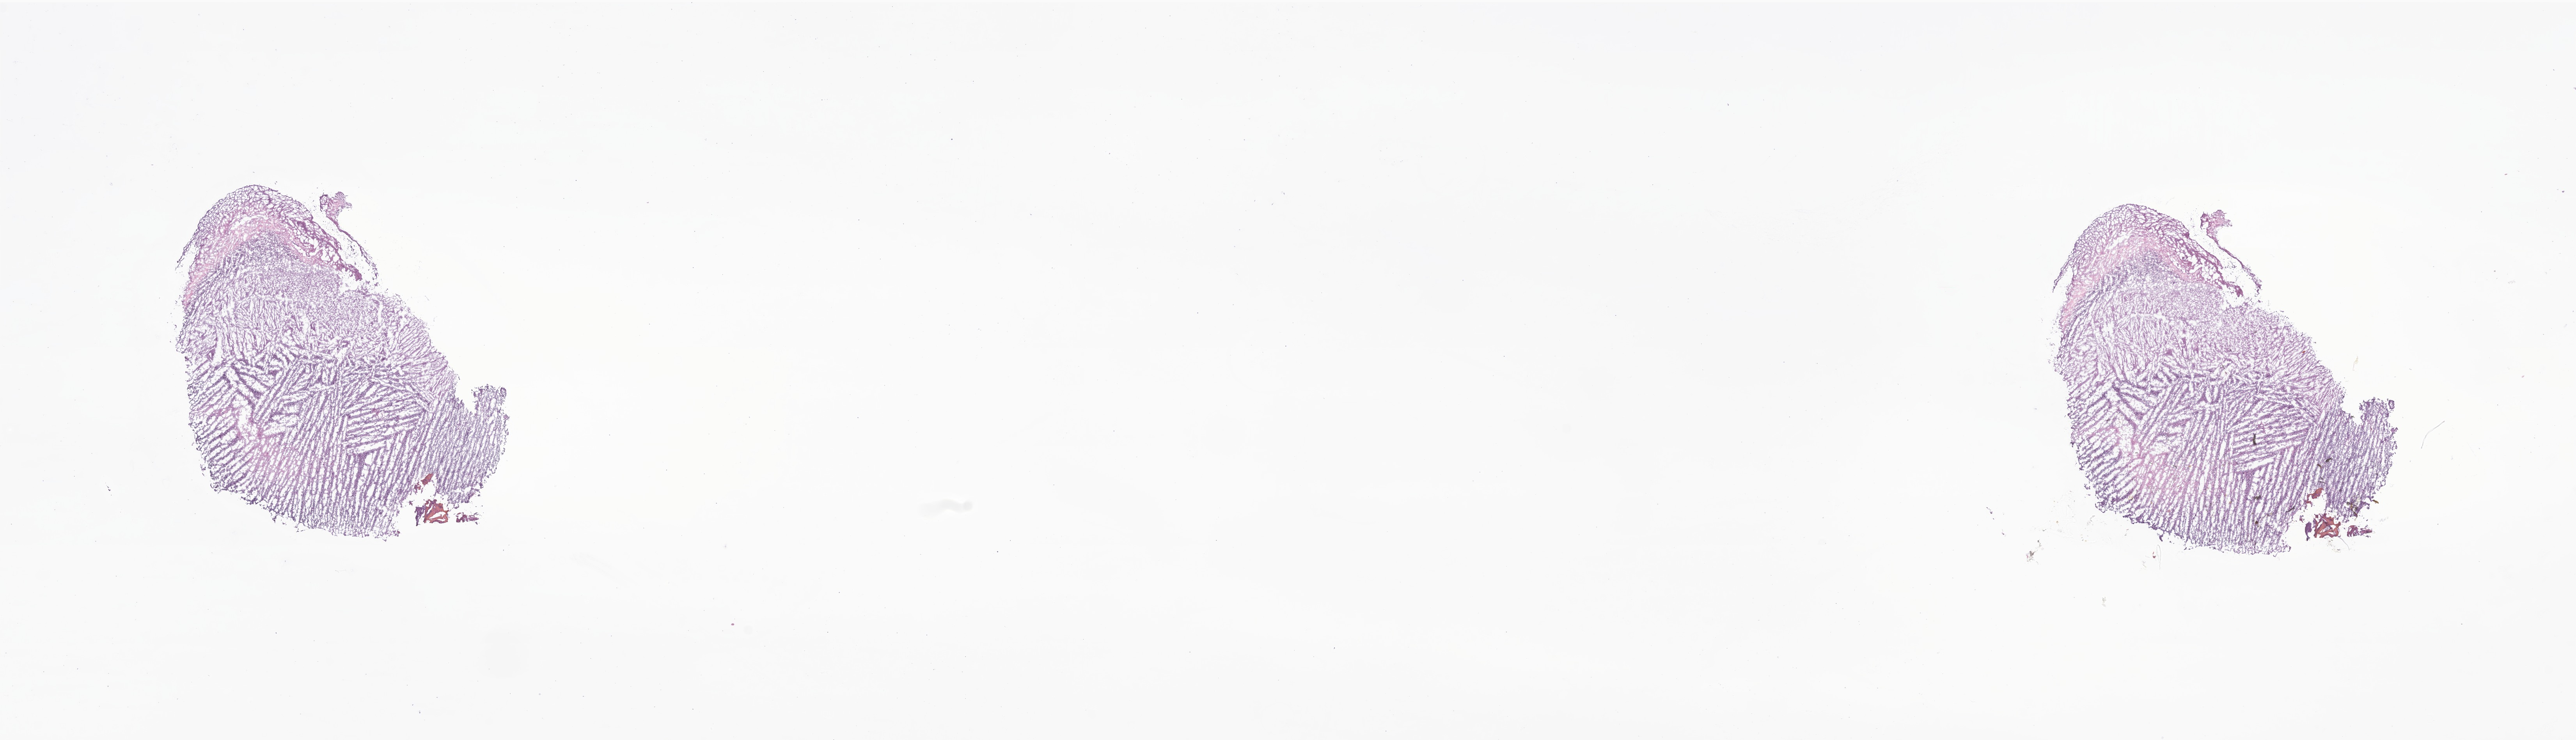
Digitized haematoxylin and eosin-stained section of tumor tissue from the brain, whole scanned area (about 27.8 x 8.0 mm) shown as a low-resolution overview, cryosection (OCT / tissue freezing medium). Patient male; age 119 months.
- diagnosis: Neoplasm, malignant